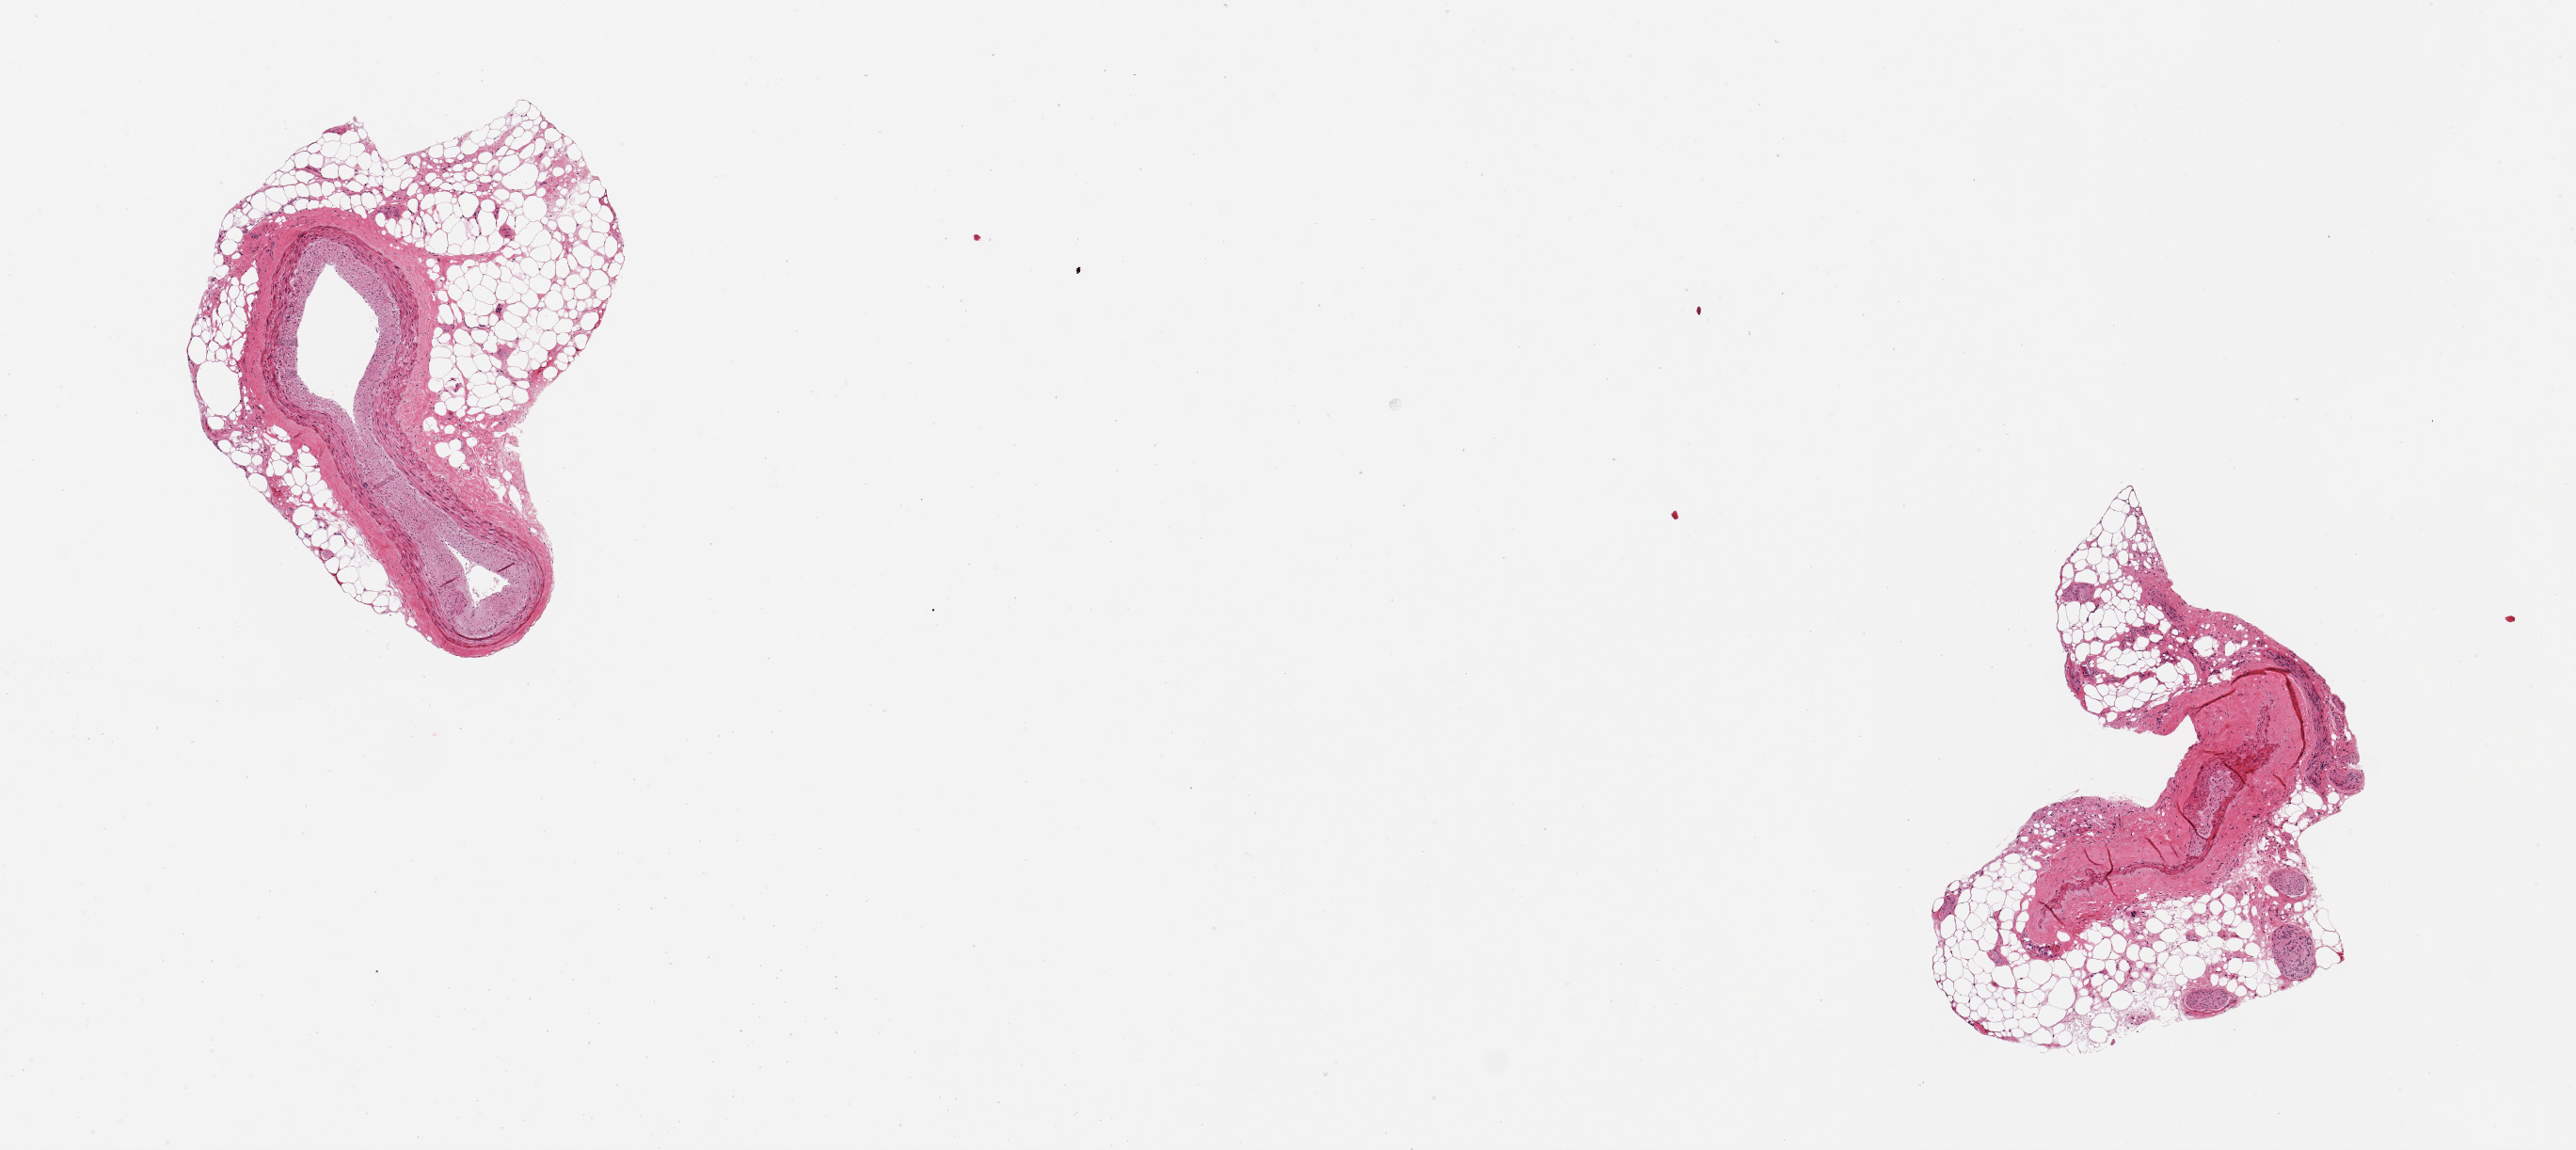
Digitized haematoxylin and eosin-stained section, a low-resolution overview of the entire scanned area, about 10.8 x 4.8 mm. PAXgene-fixed paraffin-embedded (PFPE) section. Section of coronary artery (target tissue). Tissue donor sample.
* pathologist's review note for this sample: 2 pieces. 2x2 & 2x2mm; 50% extraneous external adipose